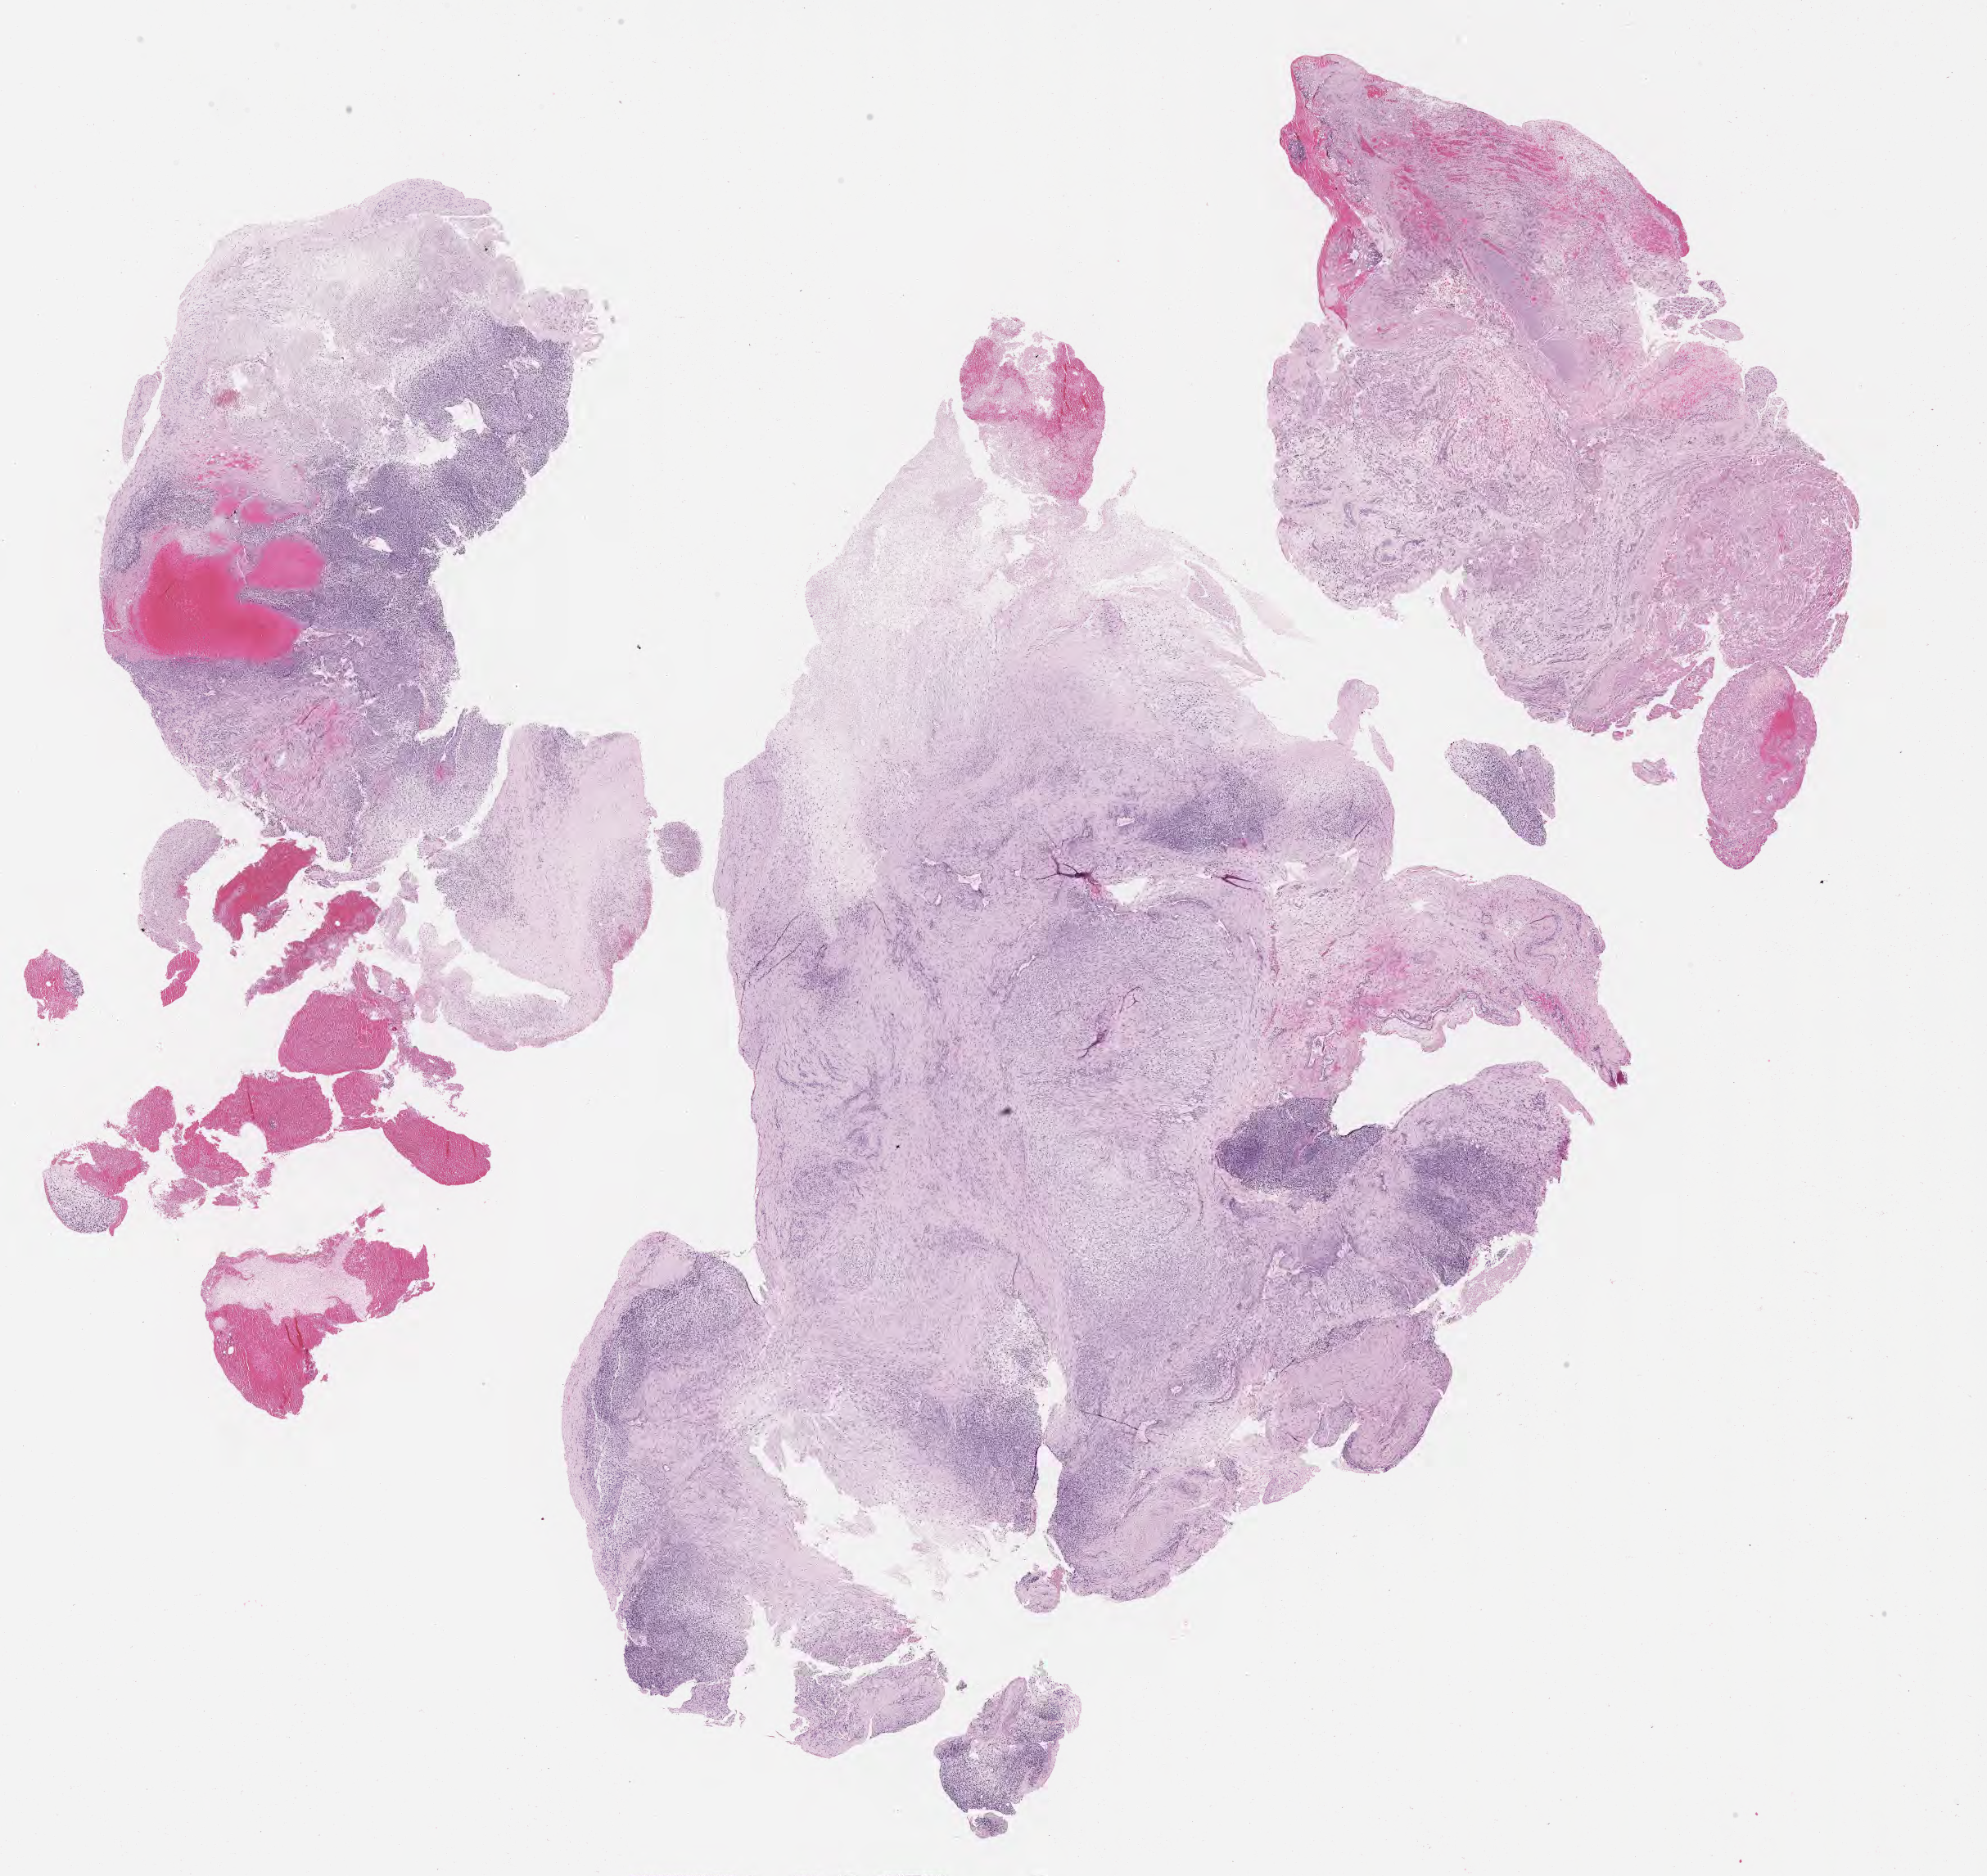
Haematoxylin and eosin whole-slide image of tumor tissue — whole scanned area (about 19.6 x 18.5 mm) shown as a low-resolution overview, FFPE section, site: soft tissue - neck, right. Male patient, age at diagnosis 4.9 years.
Diagnosis: rhabdomyosarcoma; histological classification: embryonal rhabdomyosarcoma.